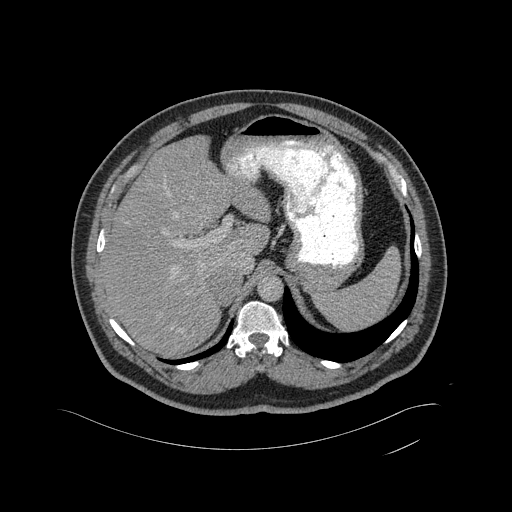
Contrast-enhanced abdominal CT, one axial slice; slice 341 of 433 in the series (ordered by position); 120 kVp; intravenous contrast given; soft-tissue window (W 400 / L 40 HU); 2 mm slice thickness; 512 × 512 image matrix, field of view 500 × 500 mm. Patient: male, 56 years. Case-level facts recorded for this patient, not image findings: diagnosis: adrenocortical carcinoma; tumour side: right adrenal; tumour size at pathology: 11.6 cm; Ki-67 index: 50 %; stage (as recorded): 3.
Structures marked on this image (semi-automatic segmentation, software-assisted and operator-edited):
- mass: bounding box [x1, y1, x2, y2] px = [211, 270, 240, 303]